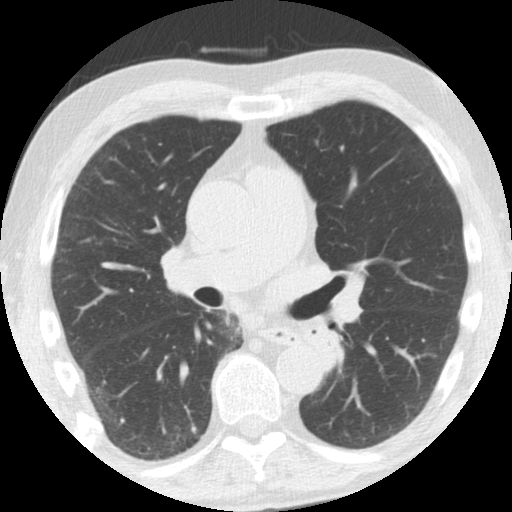
Chest CT (low-dose screening protocol), one axial image; third screening round (two years after baseline); lung window (W 1500 / L -600 HU); 120 kVp; slice 56 of 108 in the series. Male participant, aged 61 years at enrolment. Former smoker at enrolment.
Expert reader's lesion annotation, bounding box <294,316,345,362> (left, top, right, bottom; pixels). No non-calcified nodule or mass ≥4 mm was recorded by the screening reader at this exam. Official screen result: negative screen, minor abnormalities not suspicious for lung cancer. Participant outcome: lung cancer diagnosed 363 days after this screen — squamous cell carcinoma, NOS, left upper lobe, left lower lobe, well differentiated (G1), stage IIB (AJCC 6th edition), 100 mm at pathology.